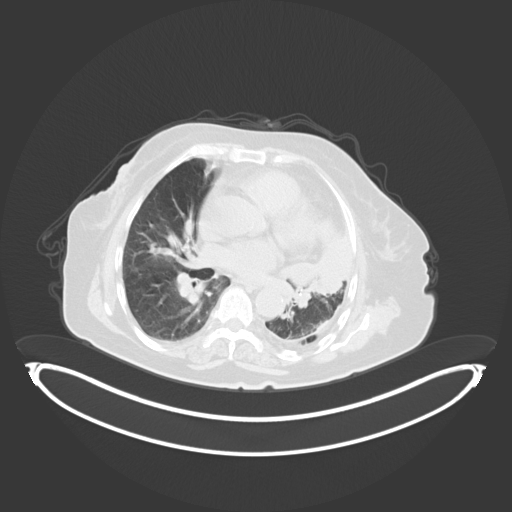
Chest CT, one axial slice. Slice 193 of 284 in the series (ordered by position). Lung window (W 1500 / L -600 HU). 3 mm slice thickness. 512 × 512 image matrix. Female patient, age 75 years. From the clinical record (not read from this slice): clinical TNM (as recorded): T3 N3 M1.
Outlined on this slice (bounding box drawn by a radiologist):
- lung tumour (recorded histology: adenocarcinoma): bounding box (x1, y1, x2, y2) in pixels: (281, 224, 359, 300)